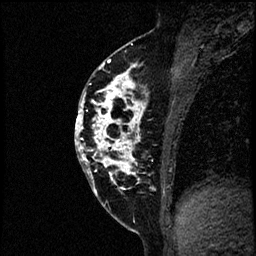
Breast MRI (dynamic contrast-enhanced), one sagittal slice; dynamic contrast-enhanced study with each time point stored as its own series, time point 2 of 4 at this slice position (early post-contrast, ordered by acquisition time); 1.5 T; TE 4.2 ms, TR 17.6 ms; 256 × 256 image matrix, field of view 200 × 200 mm. Patient: female, 40 years. From the clinical record (not read from this slice): setting: breast cancer imaged before/during neoadjuvant chemotherapy; receptor status: HER2-positive.
Structures marked on this image (semi-automatically segmented with operator editing):
- analysis volume of interest (the breast-tissue region the enhancement analysis was run in; not a lesion): bounding box <76,56,197,205> (left, top, right, bottom; pixels)
- tumour enhancement mask (voxels above the 100 % enhancement threshold inside the analysis volume of interest): <76,59,145,191>